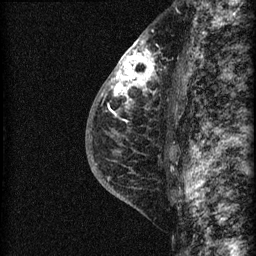
Breast MRI (dynamic contrast-enhanced), one sagittal slice; position 40 of 60 along the scan axis; dynamic contrast-enhanced series, image 2 of 3 at this slice position (ordered by acquisition); 1.5 T; TE 4.2 ms, TR 22.7 ms; 1.5 mm slice thickness; 256 × 256 image matrix. Patient: female, 48 years. Case-level facts recorded for this patient, not image findings: setting: breast cancer imaged before/during neoadjuvant chemotherapy; receptor status: triple-negative.
Structures marked on this image (semi-automatic segmentation, software-assisted and operator-edited):
- analysis volume of interest (the breast-tissue region the enhancement analysis was run in; not a lesion): bounding box (x1, y1, x2, y2) in pixels: (115, 34, 169, 162)
- tumour enhancement mask (voxels above the 90 % enhancement threshold inside the analysis volume of interest): (115, 40, 155, 117)